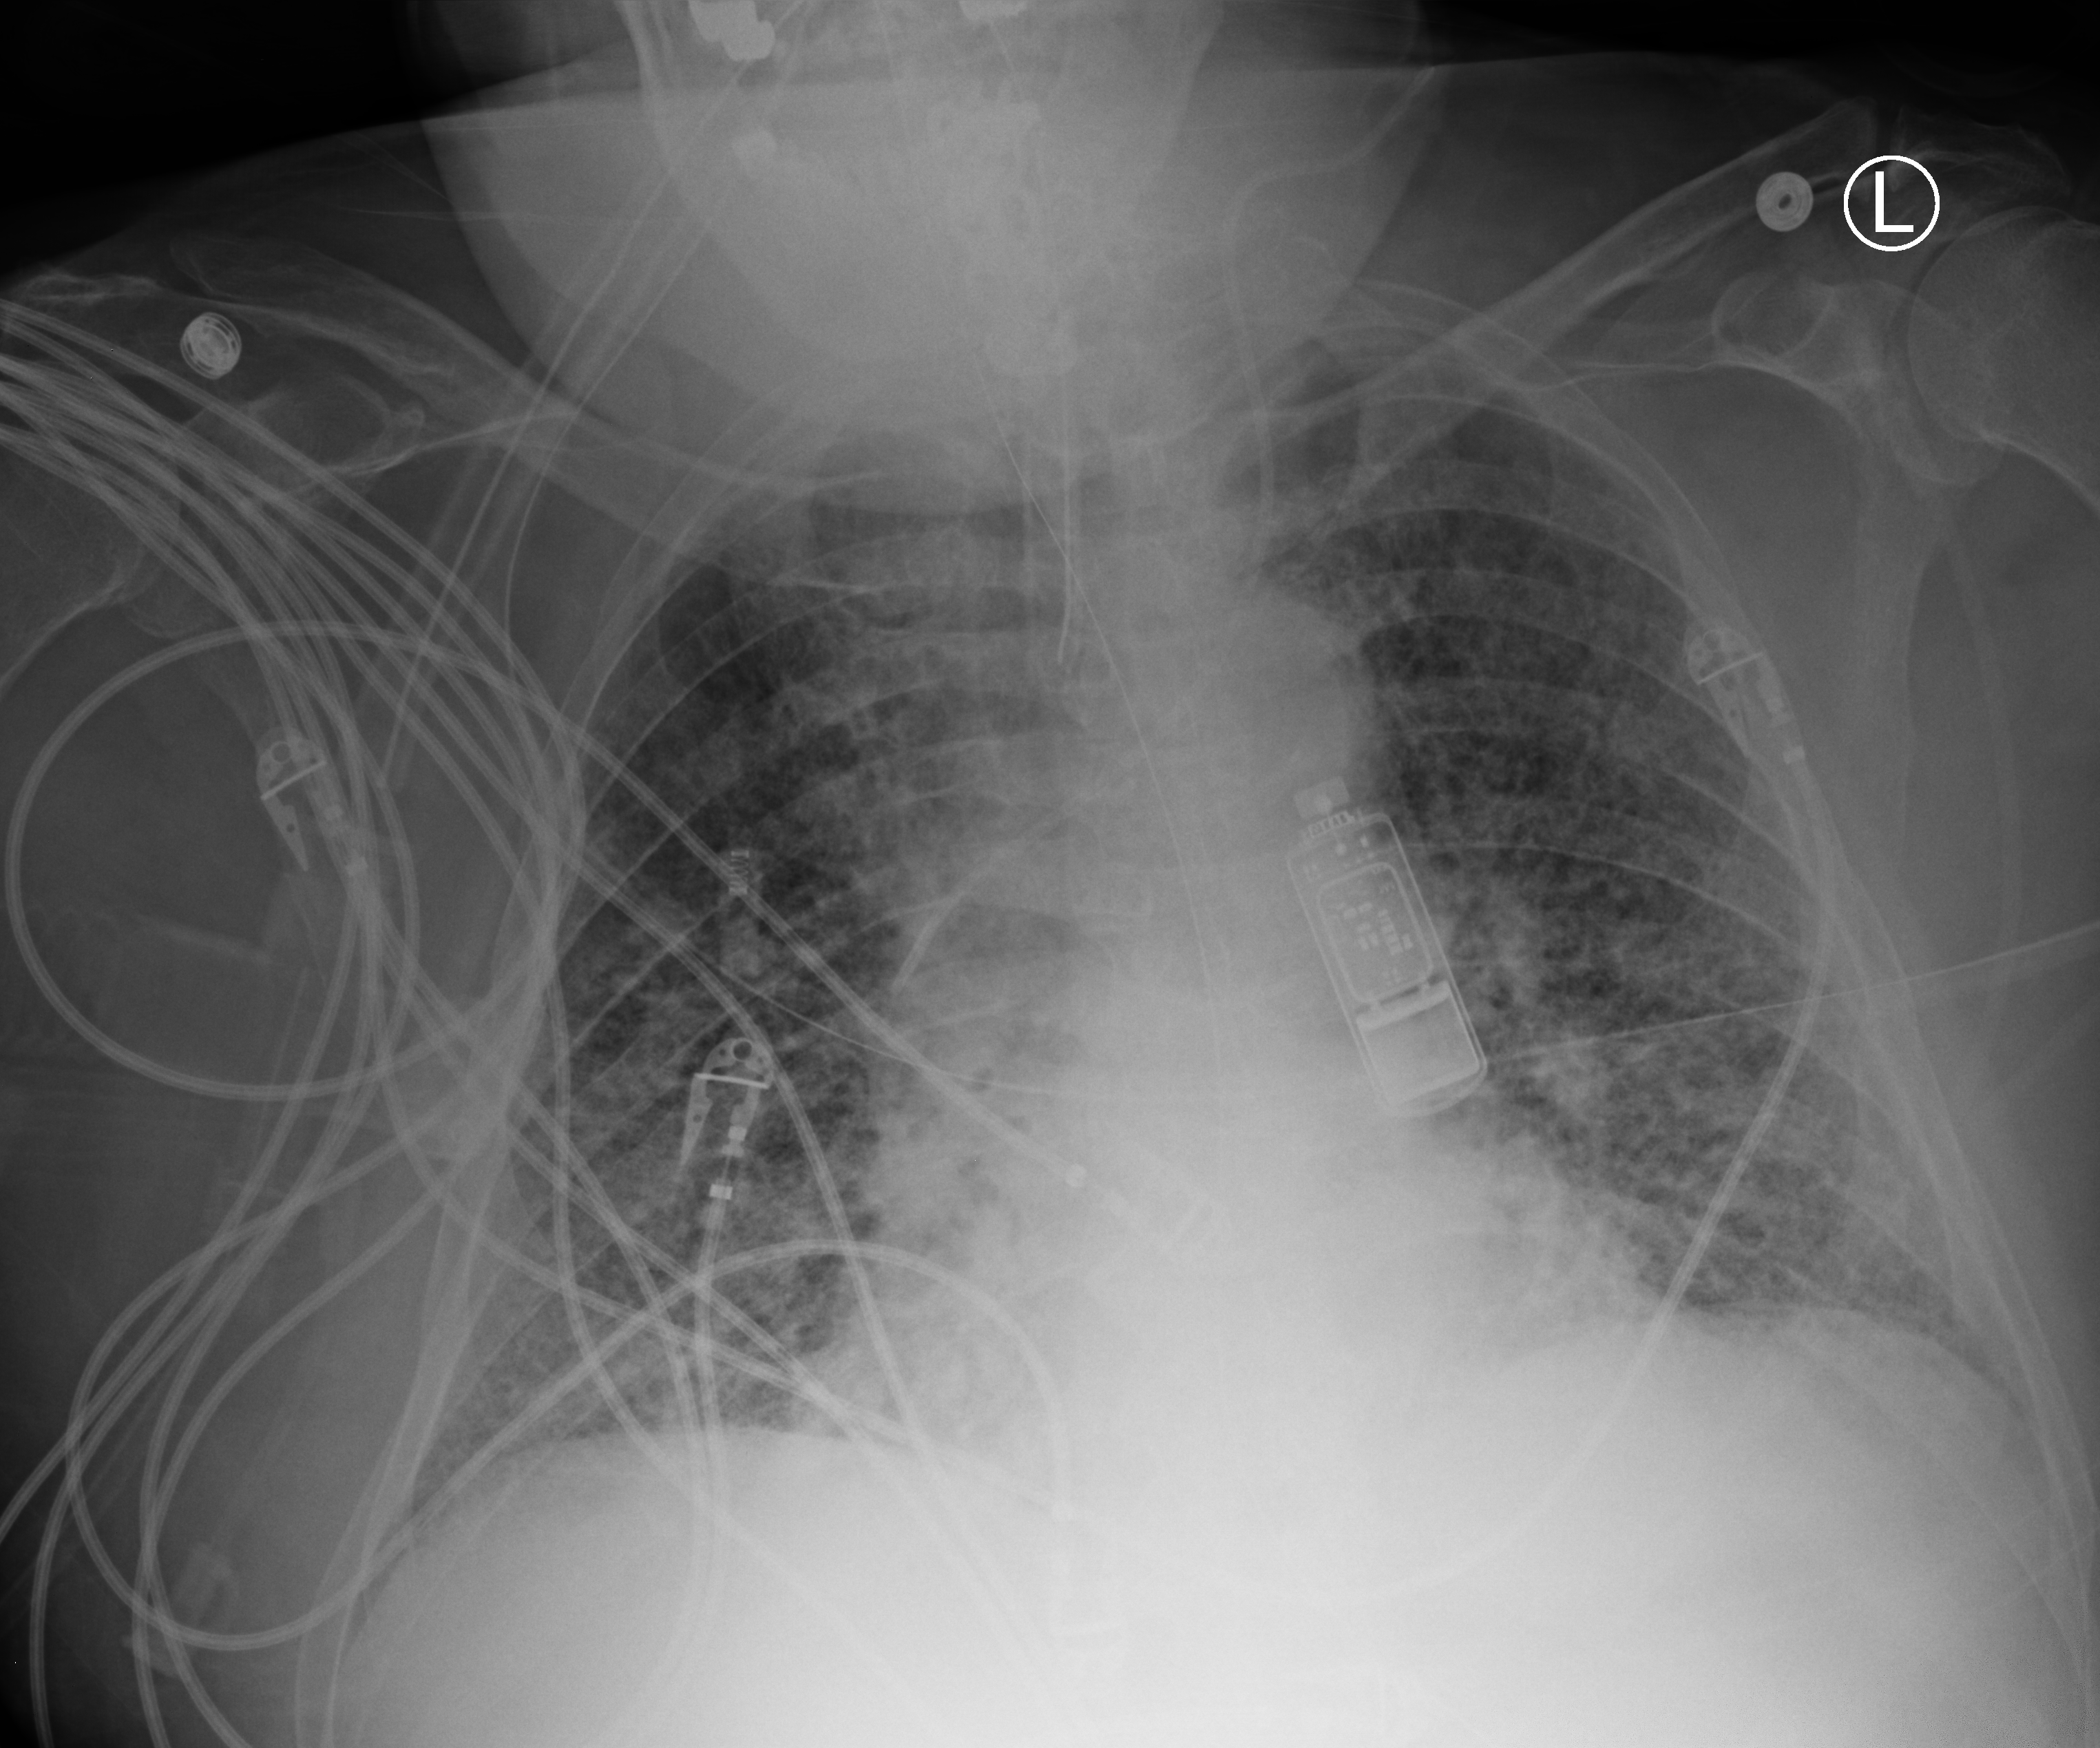
Portable chest radiograph; anteroposterior (AP) projection. Patient hospitalised with COVID-19; male, aged 60–74 years.
Hospital-stay facts (about this admission, not read from this image; timing relative to this image not recorded): diabetes (admission record): yes.